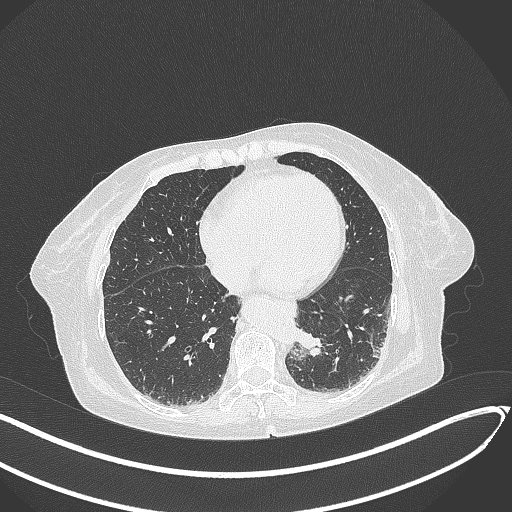
Chest CT, one axial slice. Slice 69 of 324 in the series (ordered by position). 120 kVp. Lung window (W 1500 / L -600 HU). 1 mm slice thickness. 512 × 512 image matrix, field of view 400 × 400 mm. Female patient, age 82 years. Case-level facts recorded for this patient, not image findings: clinical TNM (as recorded): T1b N0 M1.
Annotated regions visible in this slice (bounding box drawn by a radiologist):
- lung tumour (recorded histology: adenocarcinoma): bounding box (x1, y1, x2, y2) in pixels: (298, 325, 333, 363)